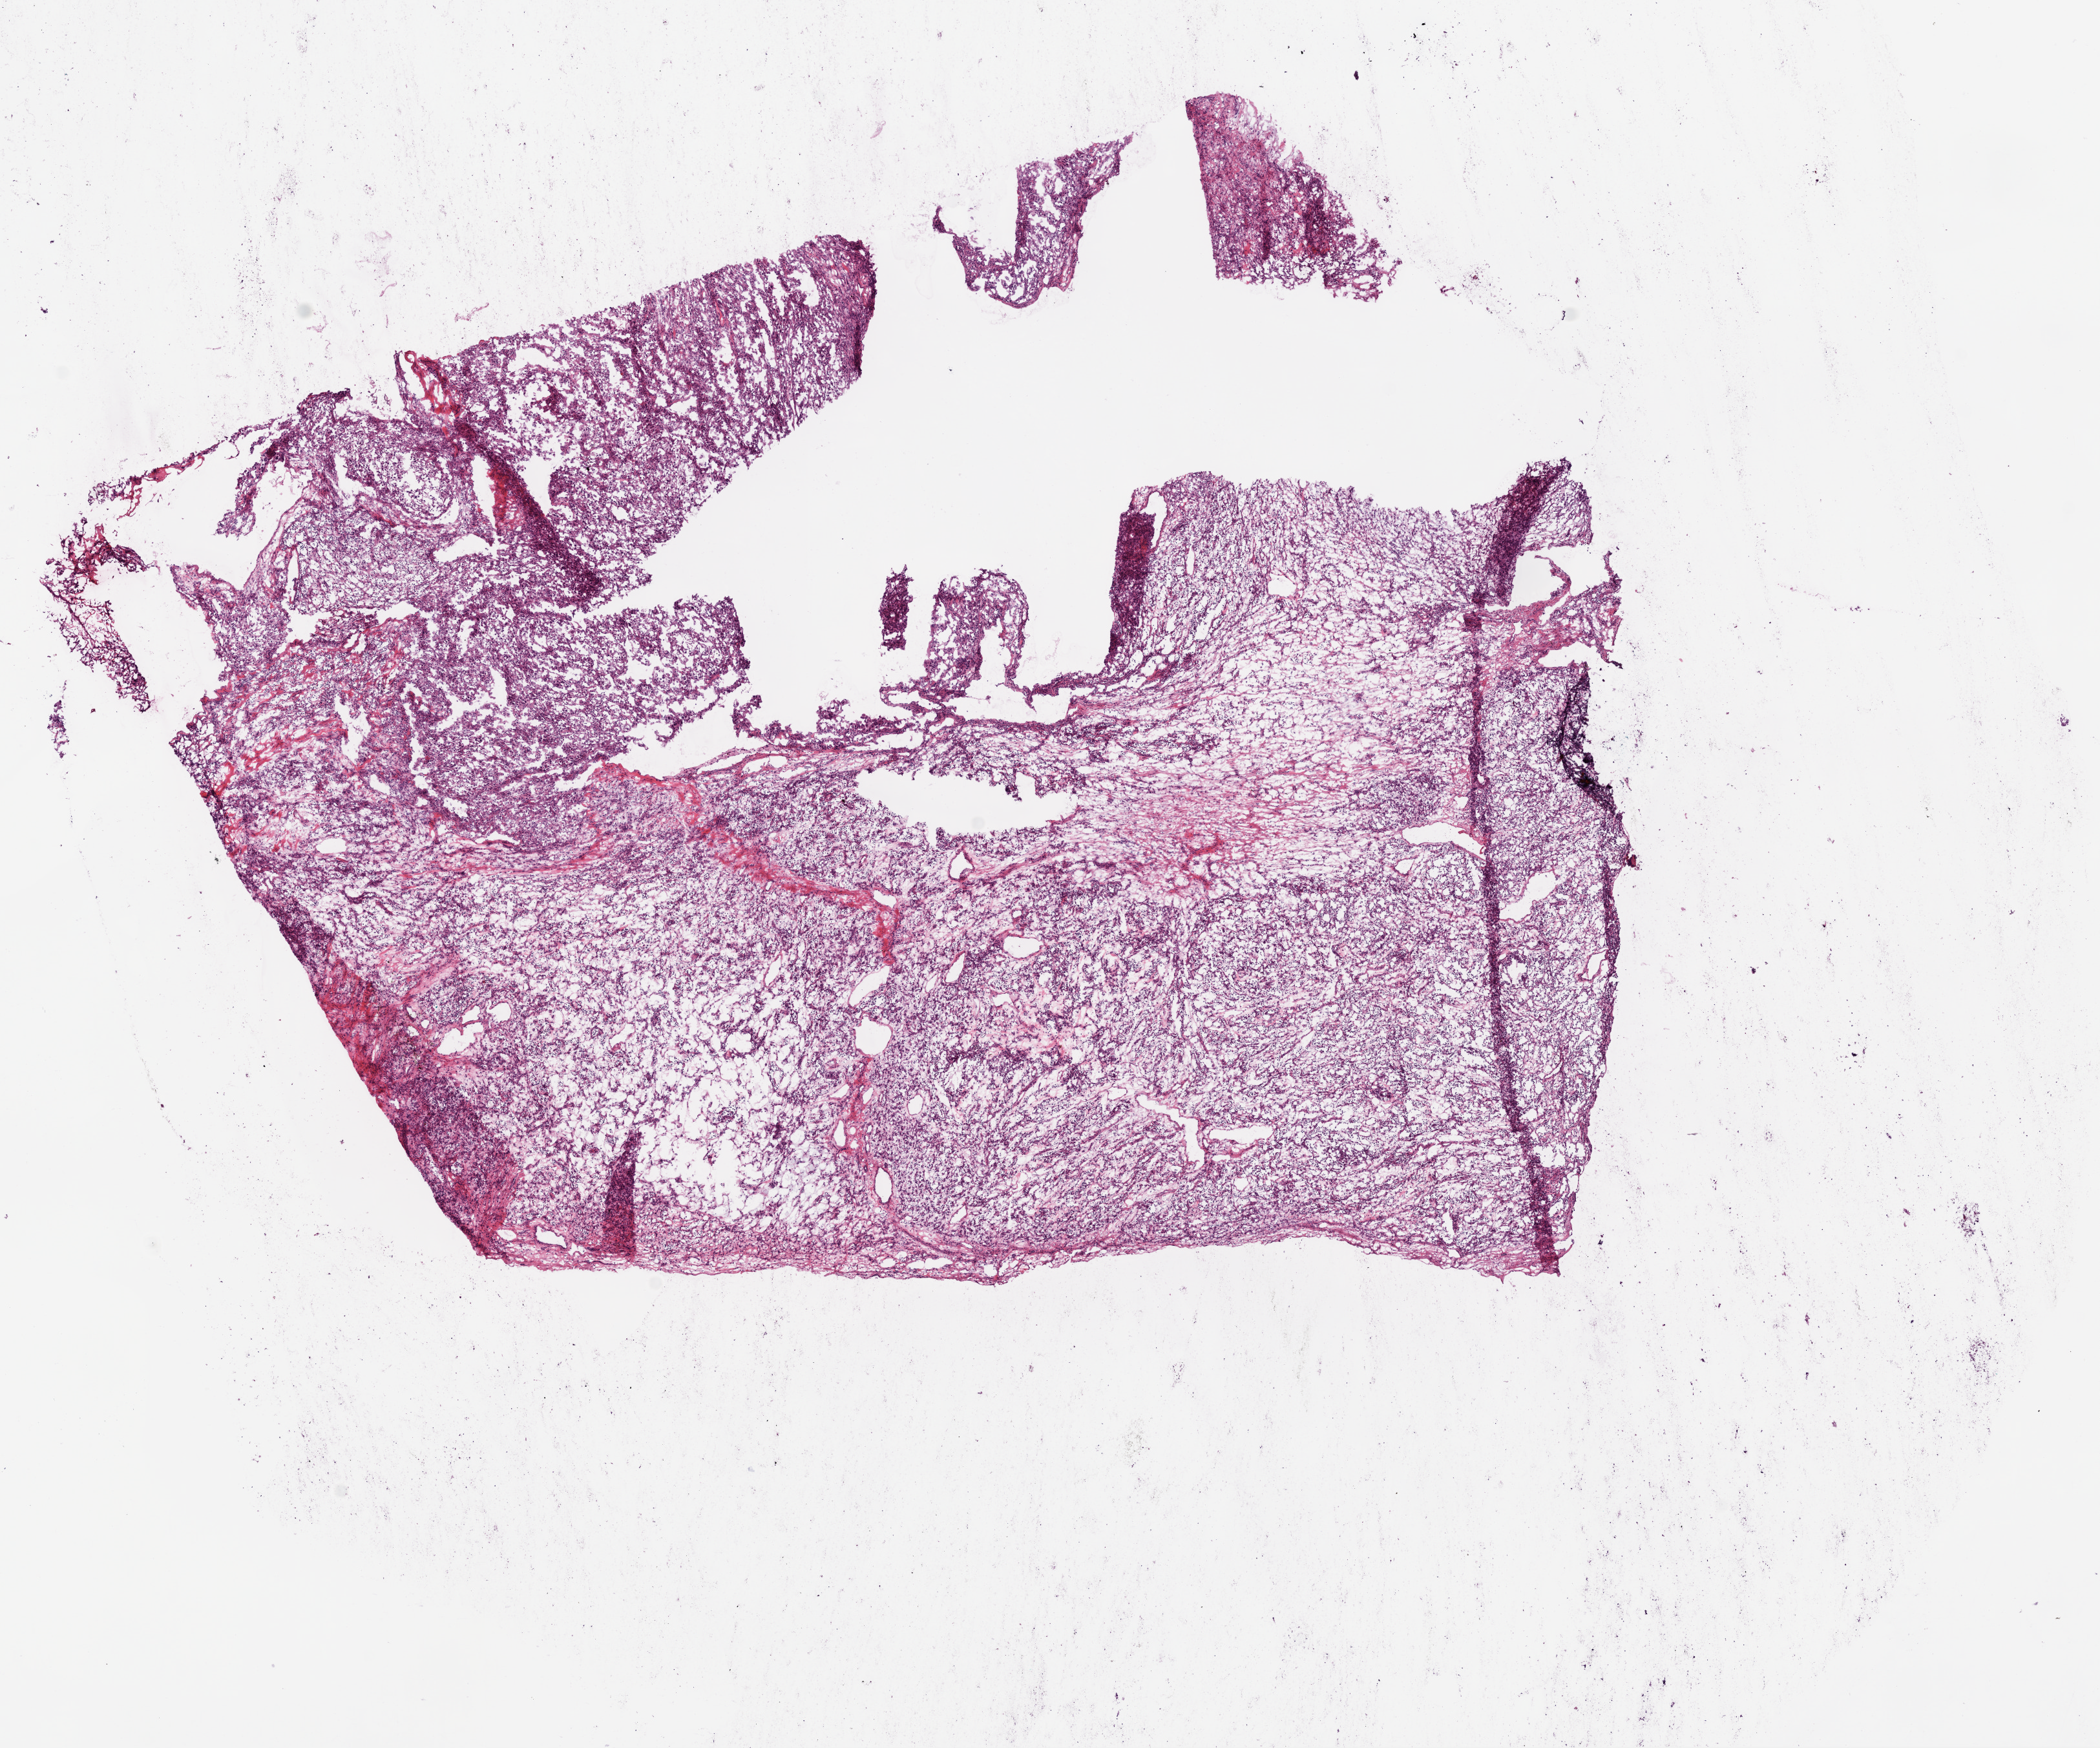
Whole-slide histology image, H&E-stained, a low-resolution overview of the entire scanned area, about 13.0 x 10.9 mm. Frozen section. Kidney, primary tumour sample. Patient: female, age at initial diagnosis 62 years. Histologic grade: G3 (poorly differentiated). Pathologist review of this section (percent, as recorded): tumour cells 90%, tumour nuclei 70%, normal cells 0%, stromal cells 10%, necrosis 0%.
• AJCC pathologic stage: II (6th edition)
• histologic diagnosis: Clear cell adenocarcinoma, NOS